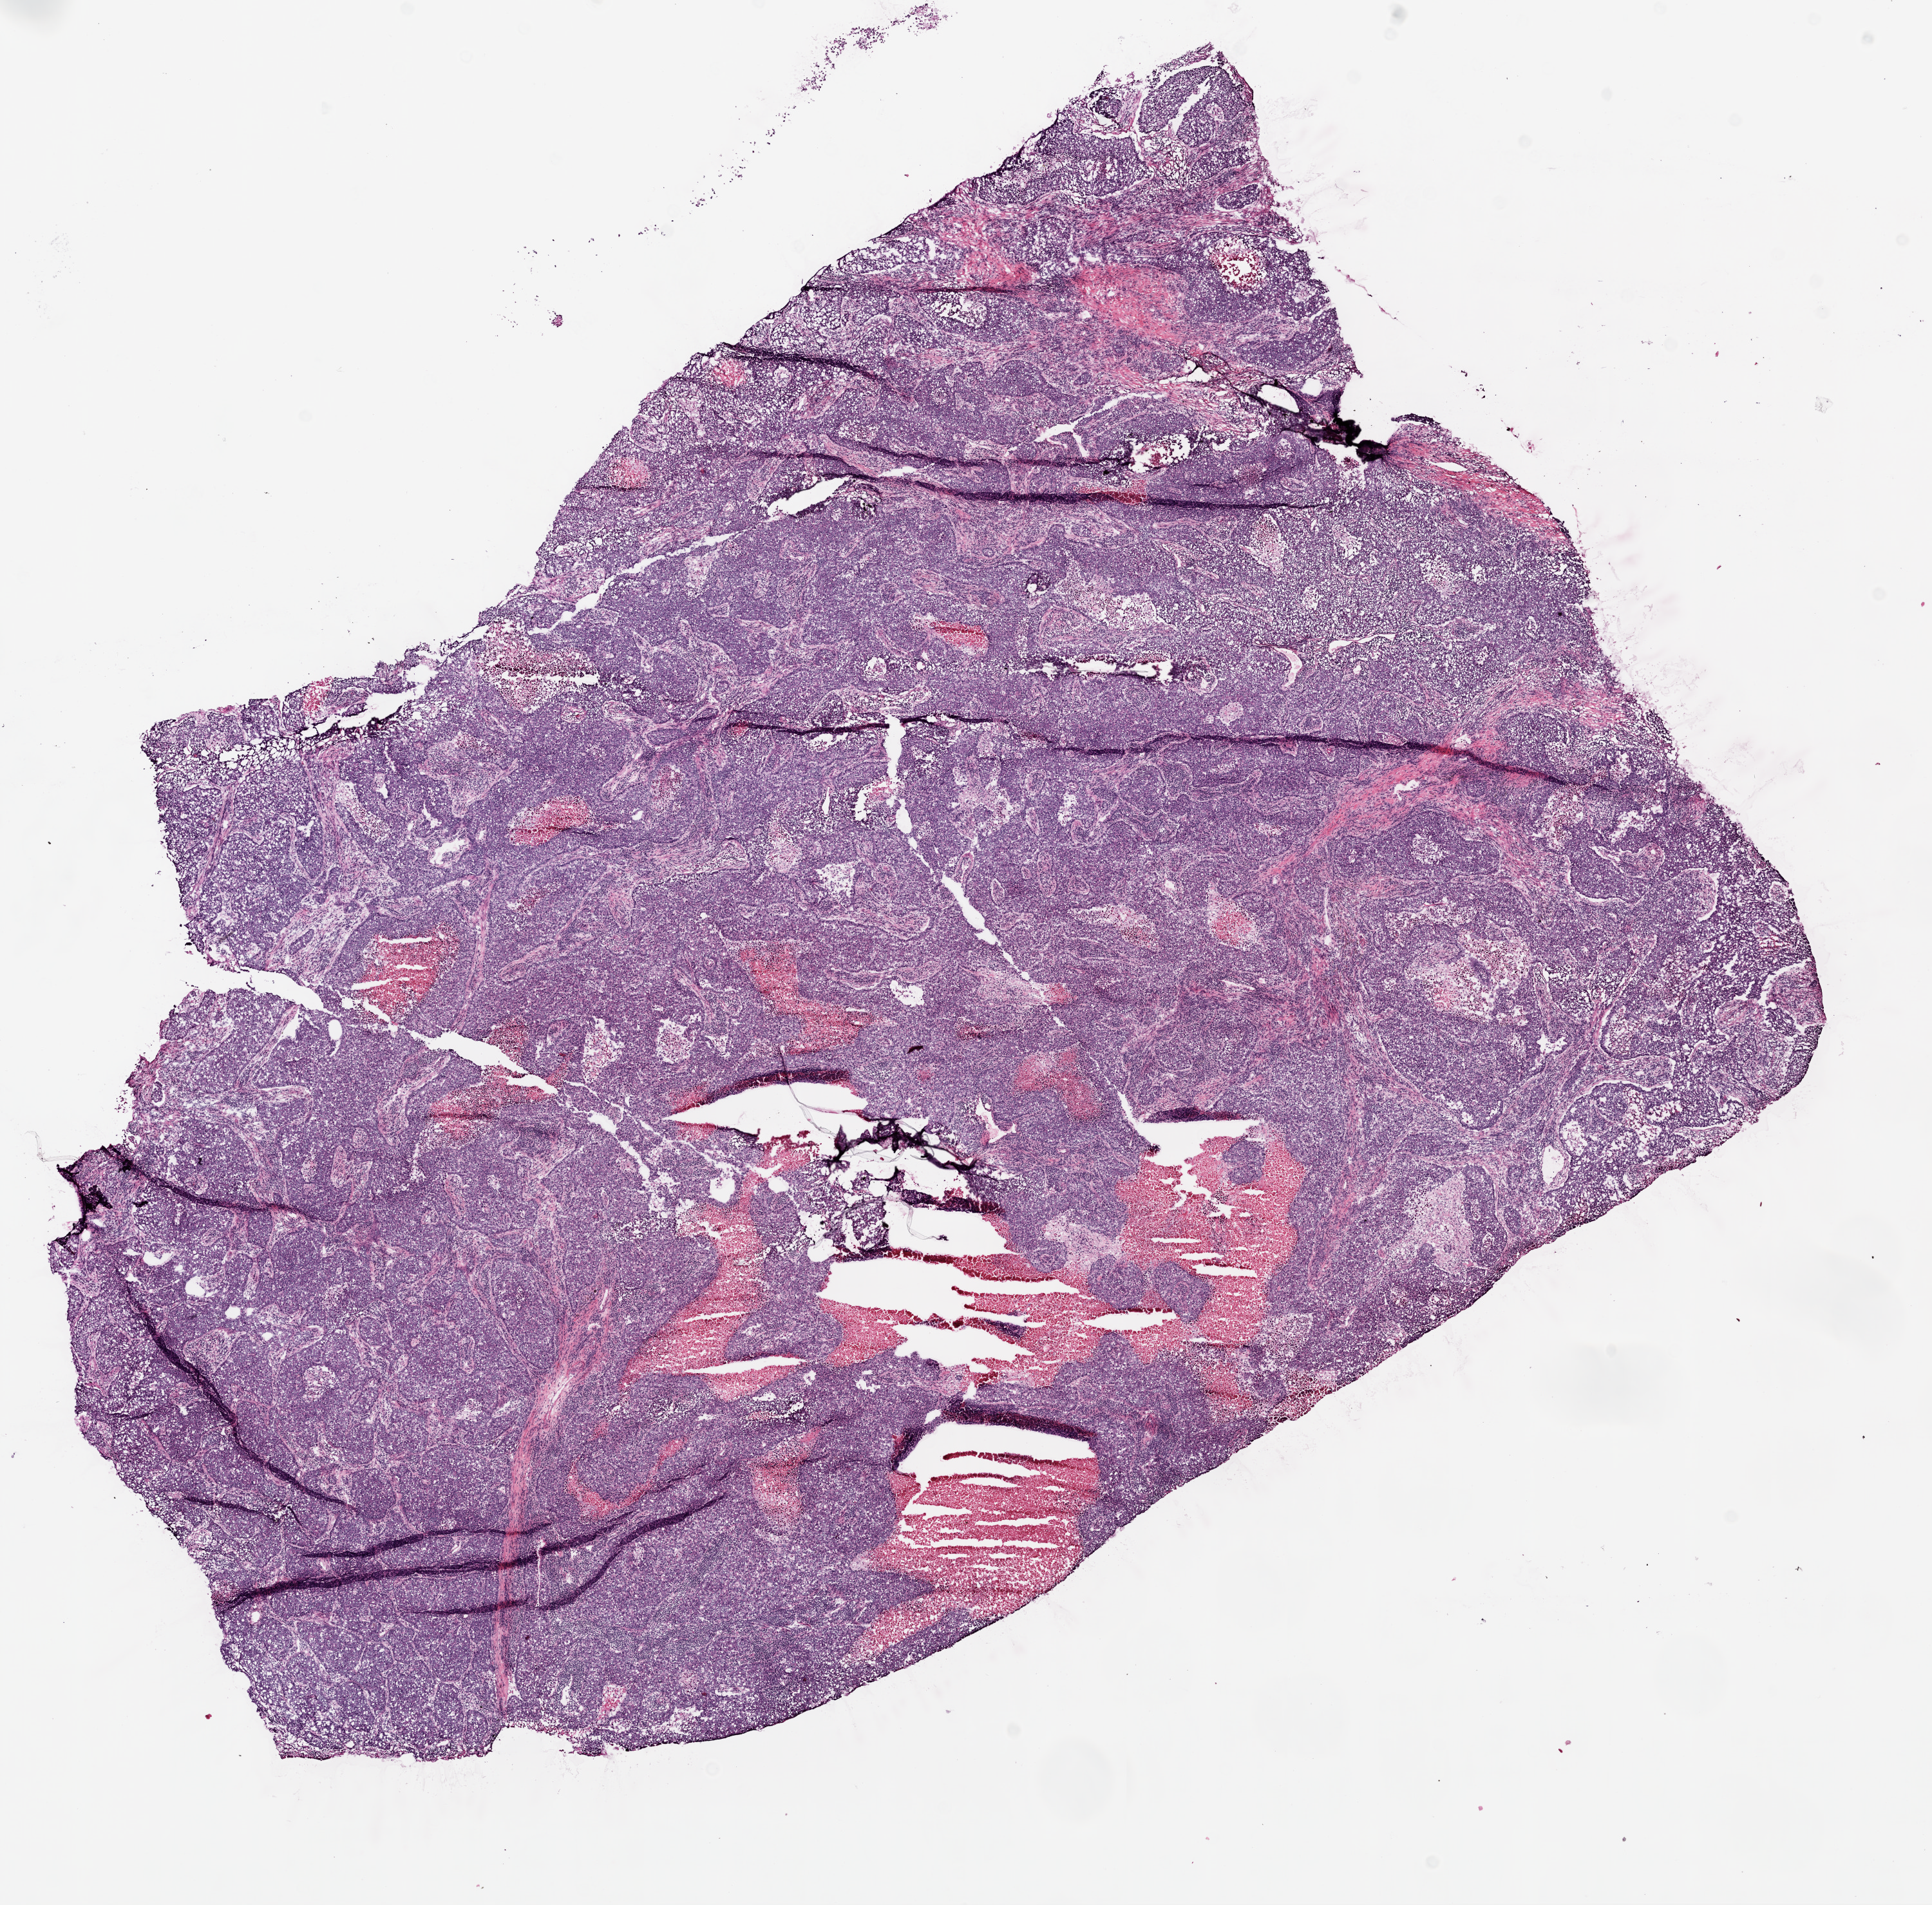
Digitized H&E-stained tissue section (whole slide) — low-resolution overview of the scanned area, about 12.0 x 11.9 mm. Frozen section from the top of the tissue portion. Sample: primary tumour, lung. Male patient; age at initial diagnosis 64 years.
Histologic diagnosis: Squamous cell carcinoma, NOS (upper lobe, lung).